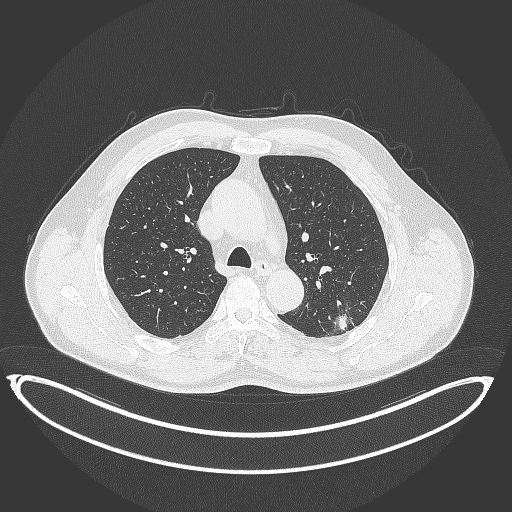
Chest CT, one axial slice; position 246 of 399 along the scan axis; lung window (W 1500 / L -600 HU); 1 mm slice thickness; 512 × 512 image matrix, field of view 469 × 469 mm. Male patient, age 58 years. Case-level facts recorded for this patient, not image findings: clinical TNM (as recorded): T1c N0 M0; histopathological grade: G1-2.
Annotated regions visible in this slice (rectangle marked by the reading radiologist):
- lung tumour (recorded histology: adenocarcinoma): bounding box <326,310,355,336> (left, top, right, bottom; pixels)